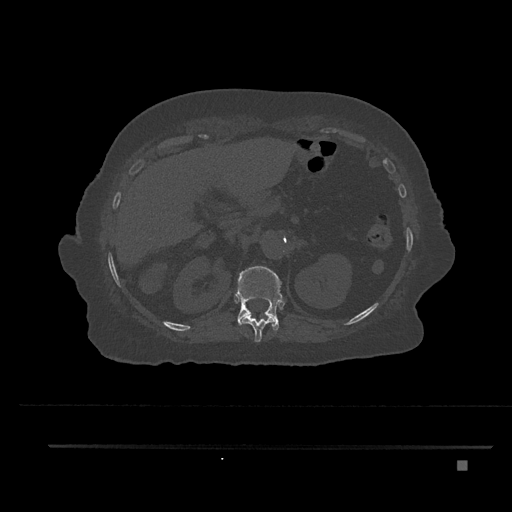
CT including the spine, one axial slice. Slice 284 of 797 in the series (ordered by position). Reconstruction kernel Br40s/3. 120 kVp. Bone window (W 1800 / L 400 HU). 512 × 512 image matrix, field of view 437 × 437 mm. Female patient, age 76 years. Case-level facts recorded for this patient, not image findings: primary cancer: lung; vertebrae with lytic lesions (as recorded): T11, L3.
Outlined on this slice (semi-automatic segmentation, software-assisted and operator-edited):
- T11 vertebra: bounding box [x1, y1, x2, y2] px = [240, 314, 275, 342]
- T12 vertebra: [237, 266, 282, 332]